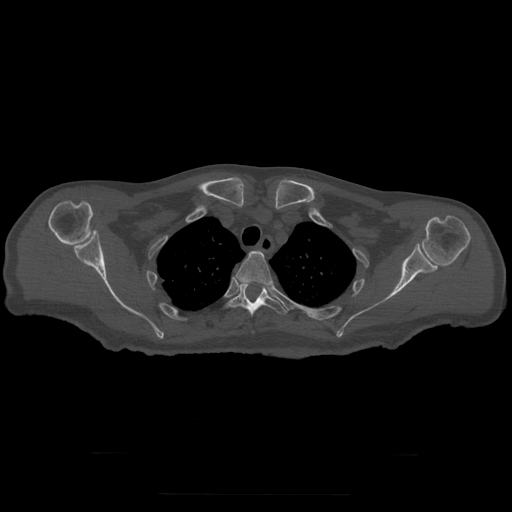
CT including the spine, one axial slice. Position 249 of 397 along the scan axis. Bone window (W 1800 / L 400 HU). 512 × 512 image matrix. Patient age 73 years. From the clinical record (not read from this slice): primary cancer: prostate.
Outlined on this slice (semi-automatically segmented with operator editing):
- T3 vertebra: bounding box (x1, y1, x2, y2) in pixels: (236, 251, 273, 288)
- T4 vertebra: (228, 283, 287, 318)